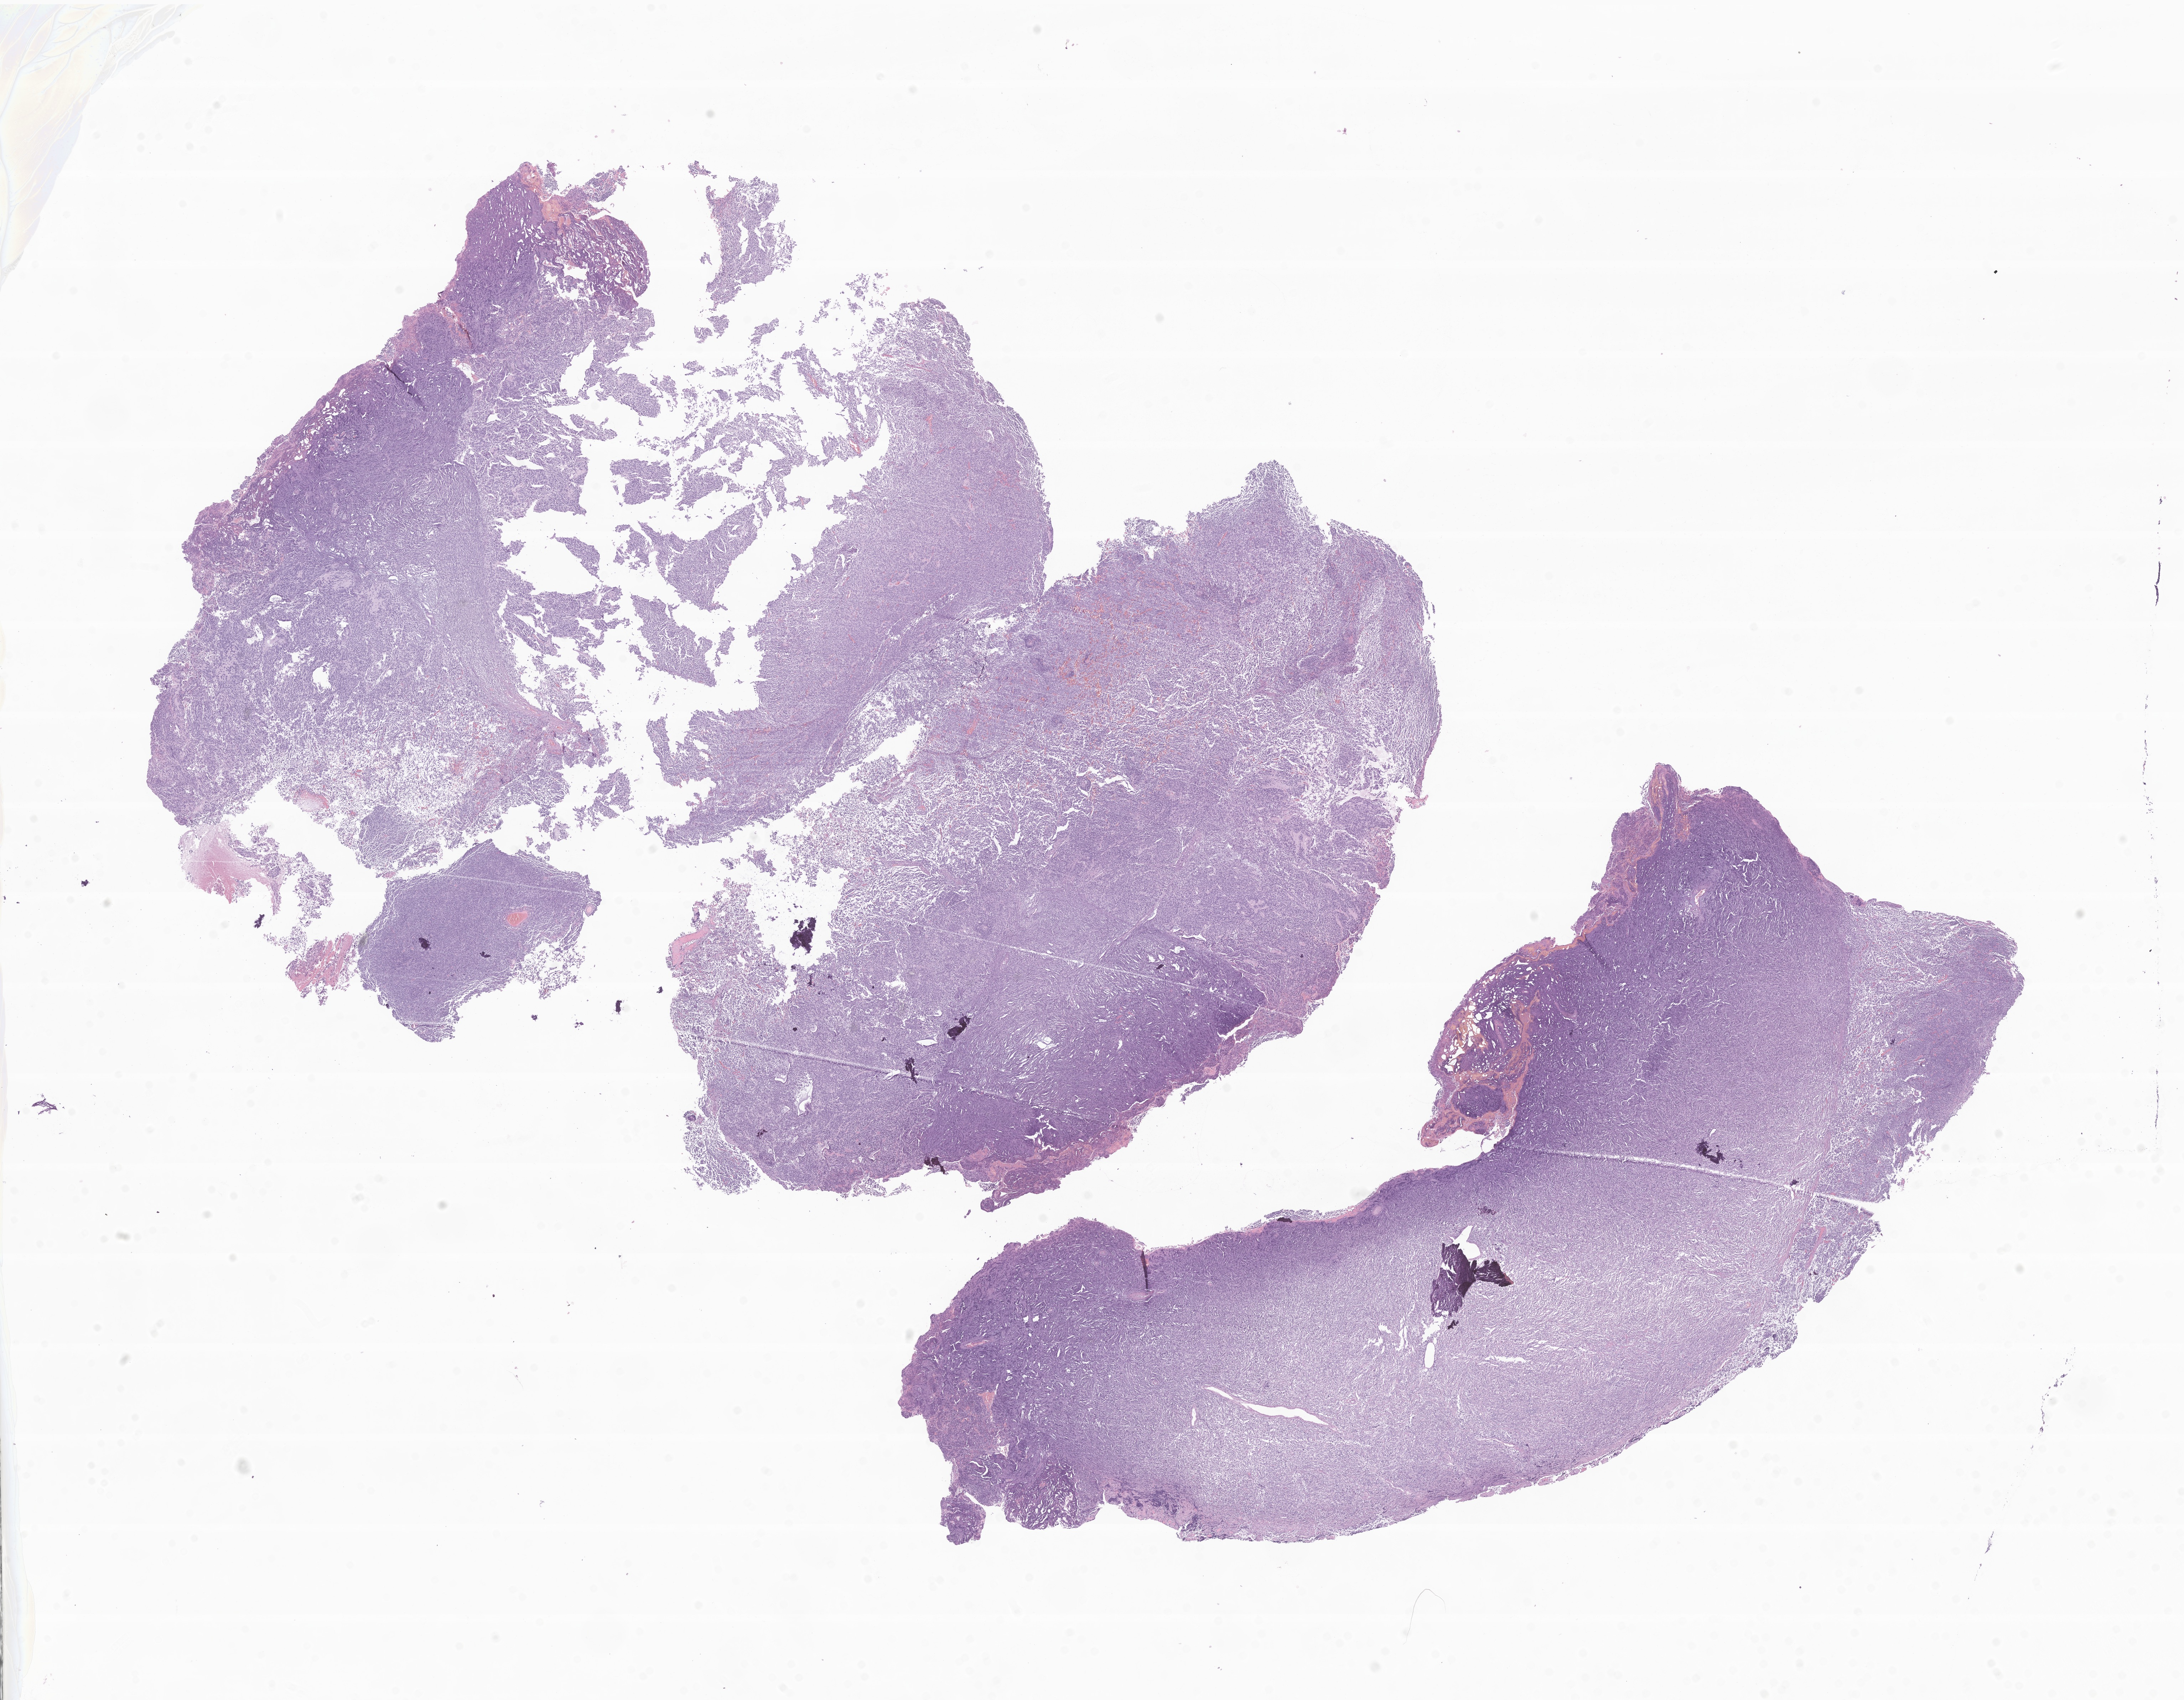
Digitized H&E-stained section of tumor tissue from the brain — a low-resolution overview of the entire scanned area, about 25.8 x 20.1 mm; FFPE section. Patient male; age 174 months.
Diagnosis: Medulloblastoma, NOS.